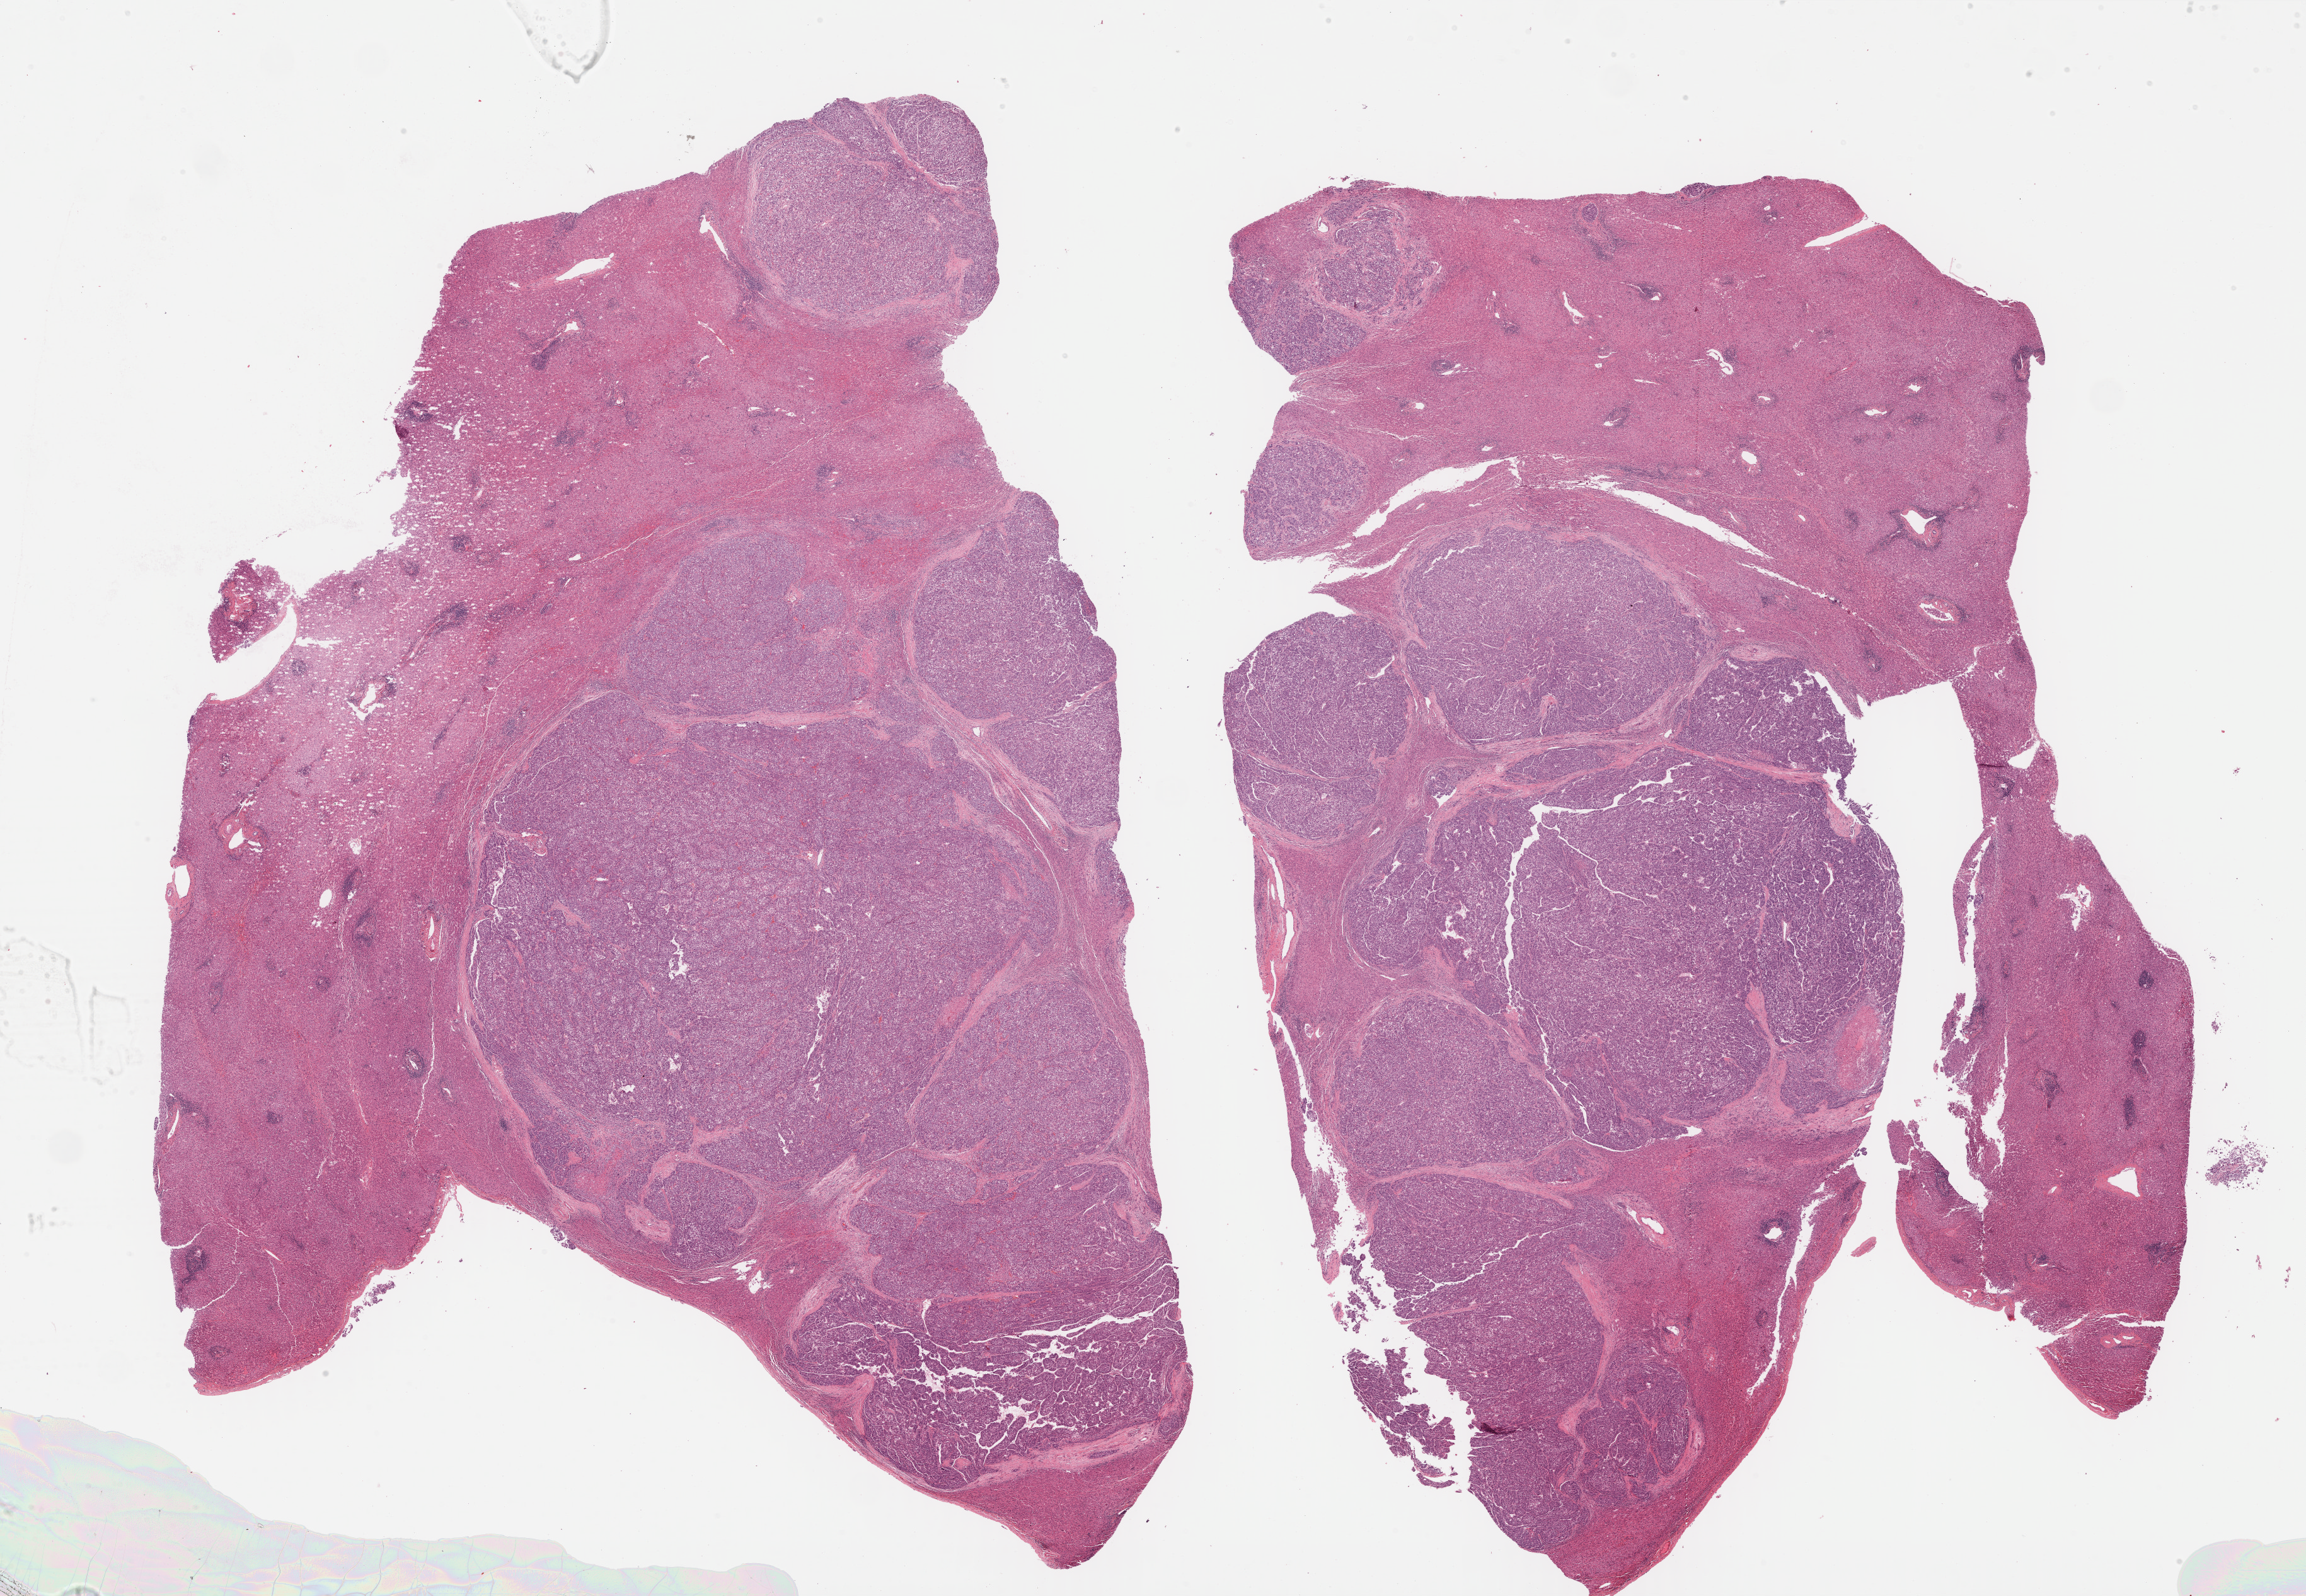
Whole-slide histology image, Hematoxylin and eosin (H&E) stained — shown as a low-resolution overview of the whole scanned area (about 29.6 x 20.5 mm), formalin-fixed paraffin-embedded (FFPE) diagnostic section, sample: primary tumour, liver. Patient: female, age at initial diagnosis 65 years. Histologic grade: G3 (poorly differentiated).
- diagnosis: Hepatocellular carcinoma, NOS
- TNM: T3b N0 M0
- AJCC pathologic stage: IIIB (7th edition)